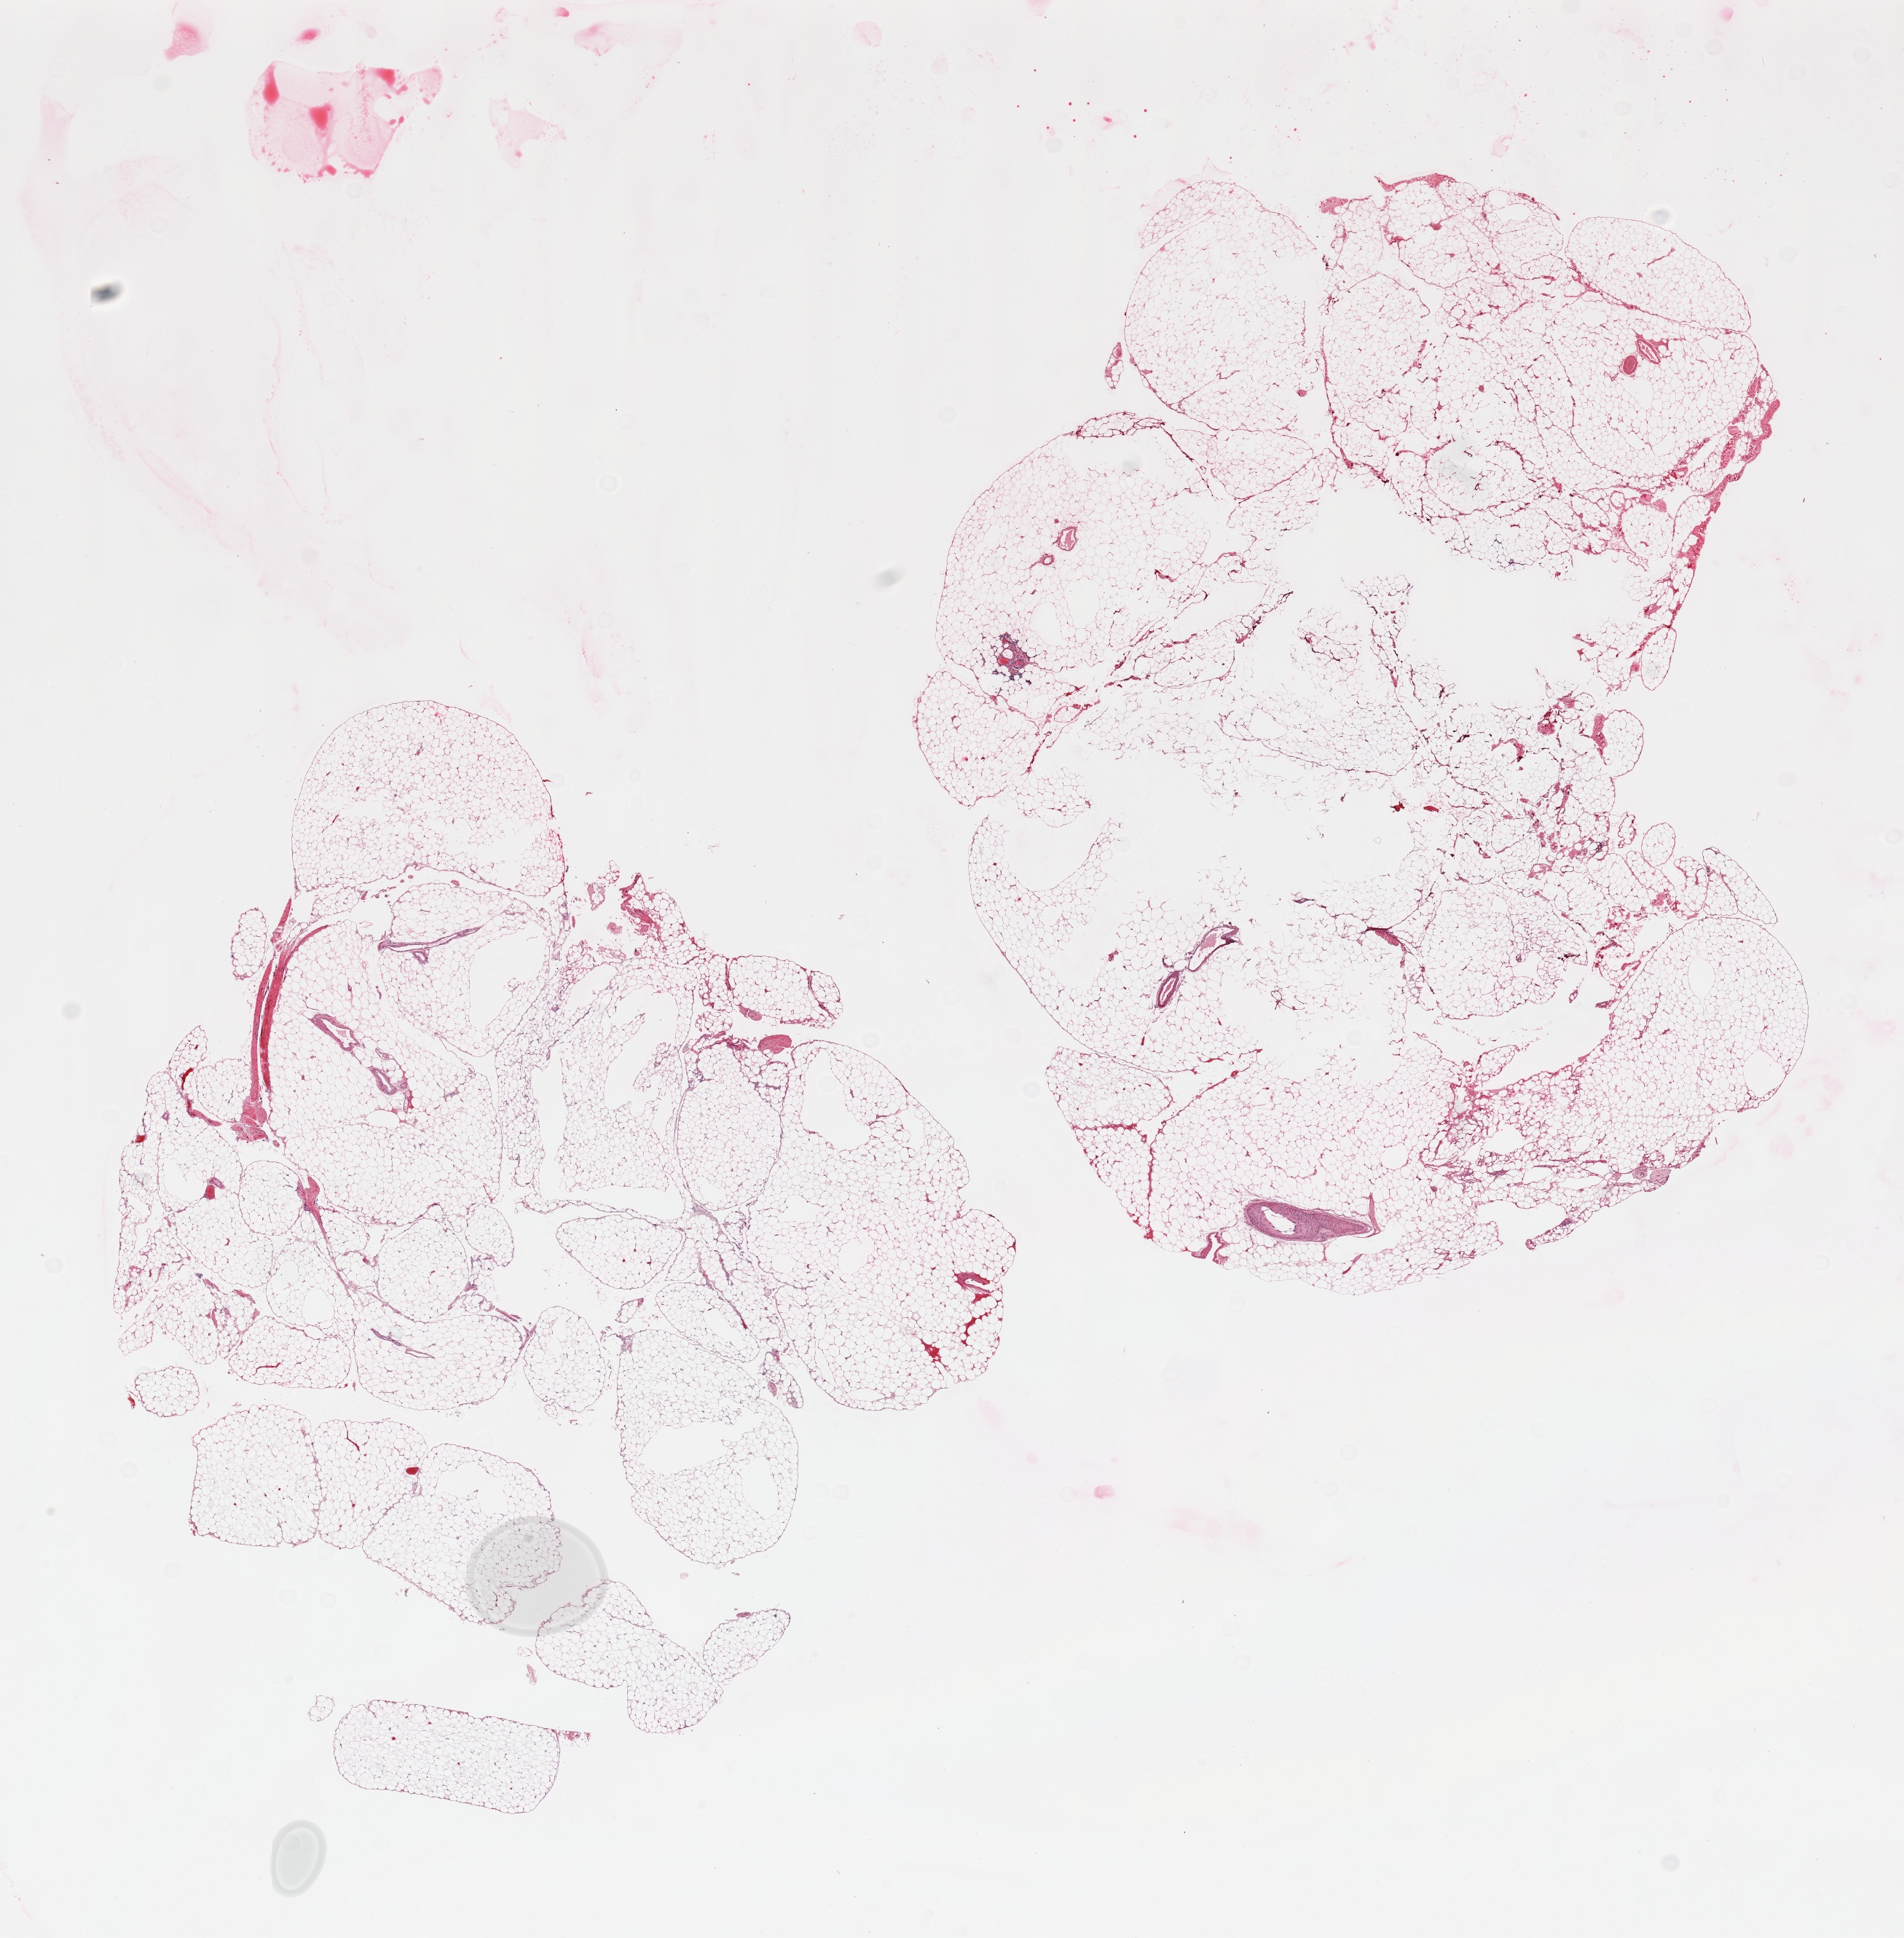
H&E whole-slide image, brightfield — shown as a low-resolution overview of the whole scanned area (about 20.7 x 21.0 mm, from a 20x scan), PAXgene-fixed paraffin-embedded (PFPE) section, section of omentum (target tissue), donor tissue sample. Donor sex: female.
Review note (as recorded): 2 pieces, adipose tissue with few larger vessels(<5%).